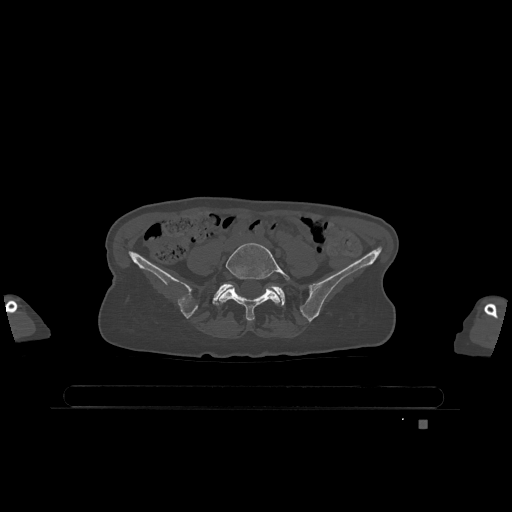
CT including the spine, one axial slice. Position 231 of 1317 along the scan axis. Bone window (W 1800 / L 400 HU). 0.5 mm slice thickness. 512 × 512 image matrix, field of view 500 × 500 mm. Patient: female, 74 years. From the clinical record (not read from this slice): primary cancer: lung.
Structures marked on this image (semi-automatic segmentation, software-assisted and operator-edited):
- L5 vertebra: bounding box [x1, y1, x2, y2] px = [217, 243, 290, 321]